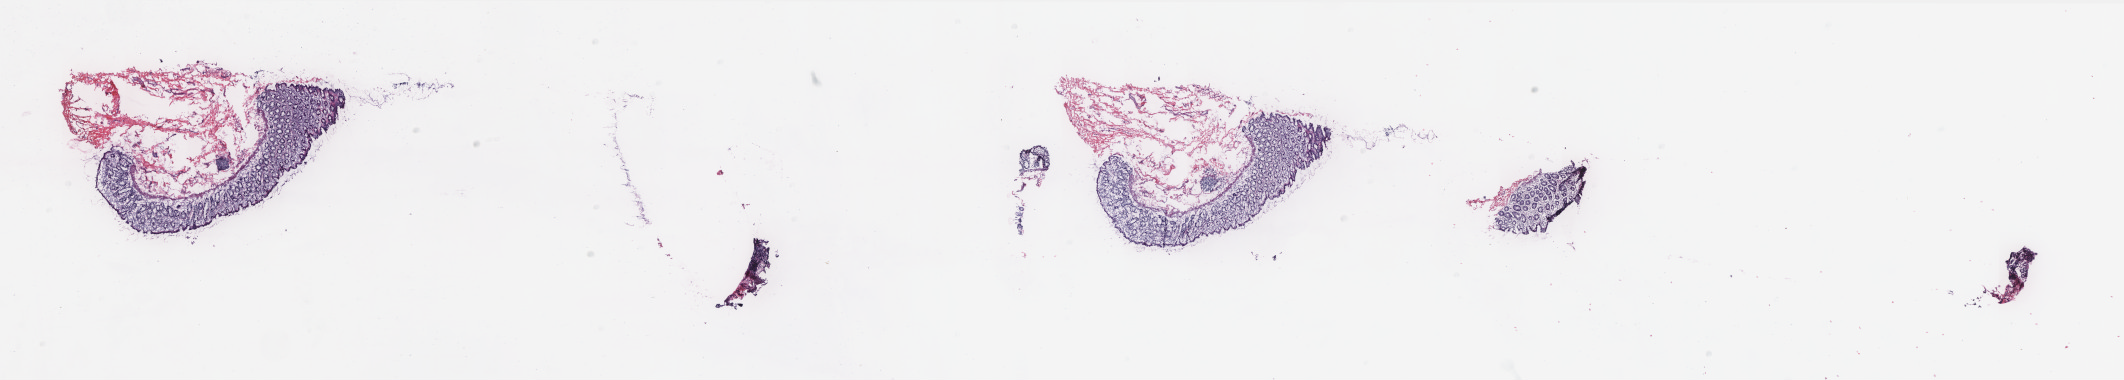
Digitized H&E tissue section (whole slide), whole scanned area (about 33.9 x 6.1 mm) shown as a low-resolution overview; frozen section from the top of the tissue portion; solid tissue normal (non-tumour tissue) sample from the rectum. Male, age 67 years at initial diagnosis. Pathologist review of this section (percent, as recorded): tumour cells 0%, normal cells 100%. Infiltration values recorded for this section: lymphocyte infiltration 35%, monocyte infiltration 7%, neutrophil infiltration 0%.
This section: solid tissue normal (non-tumour) sample from the same patient. Patient diagnosis: Adenocarcinoma, NOS.